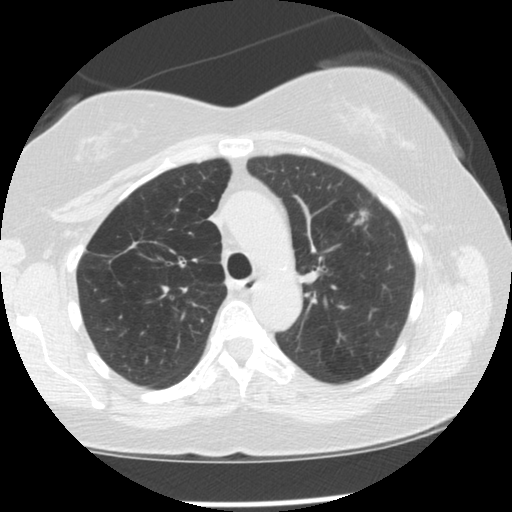
Low-dose screening chest CT, one axial slice. Position 90 of 128 along the scan axis. Reconstruction kernel STANDARD. 120 kVp. Lung window (W 1500 / L -600 HU). 512 × 512 image matrix, field of view 319 × 319 mm.
Outlined on this slice (expert manual segmentation):
- lesion 1 (tumor, upper lobe of left lung): bounding box <352,208,370,225> (left, top, right, bottom; pixels)